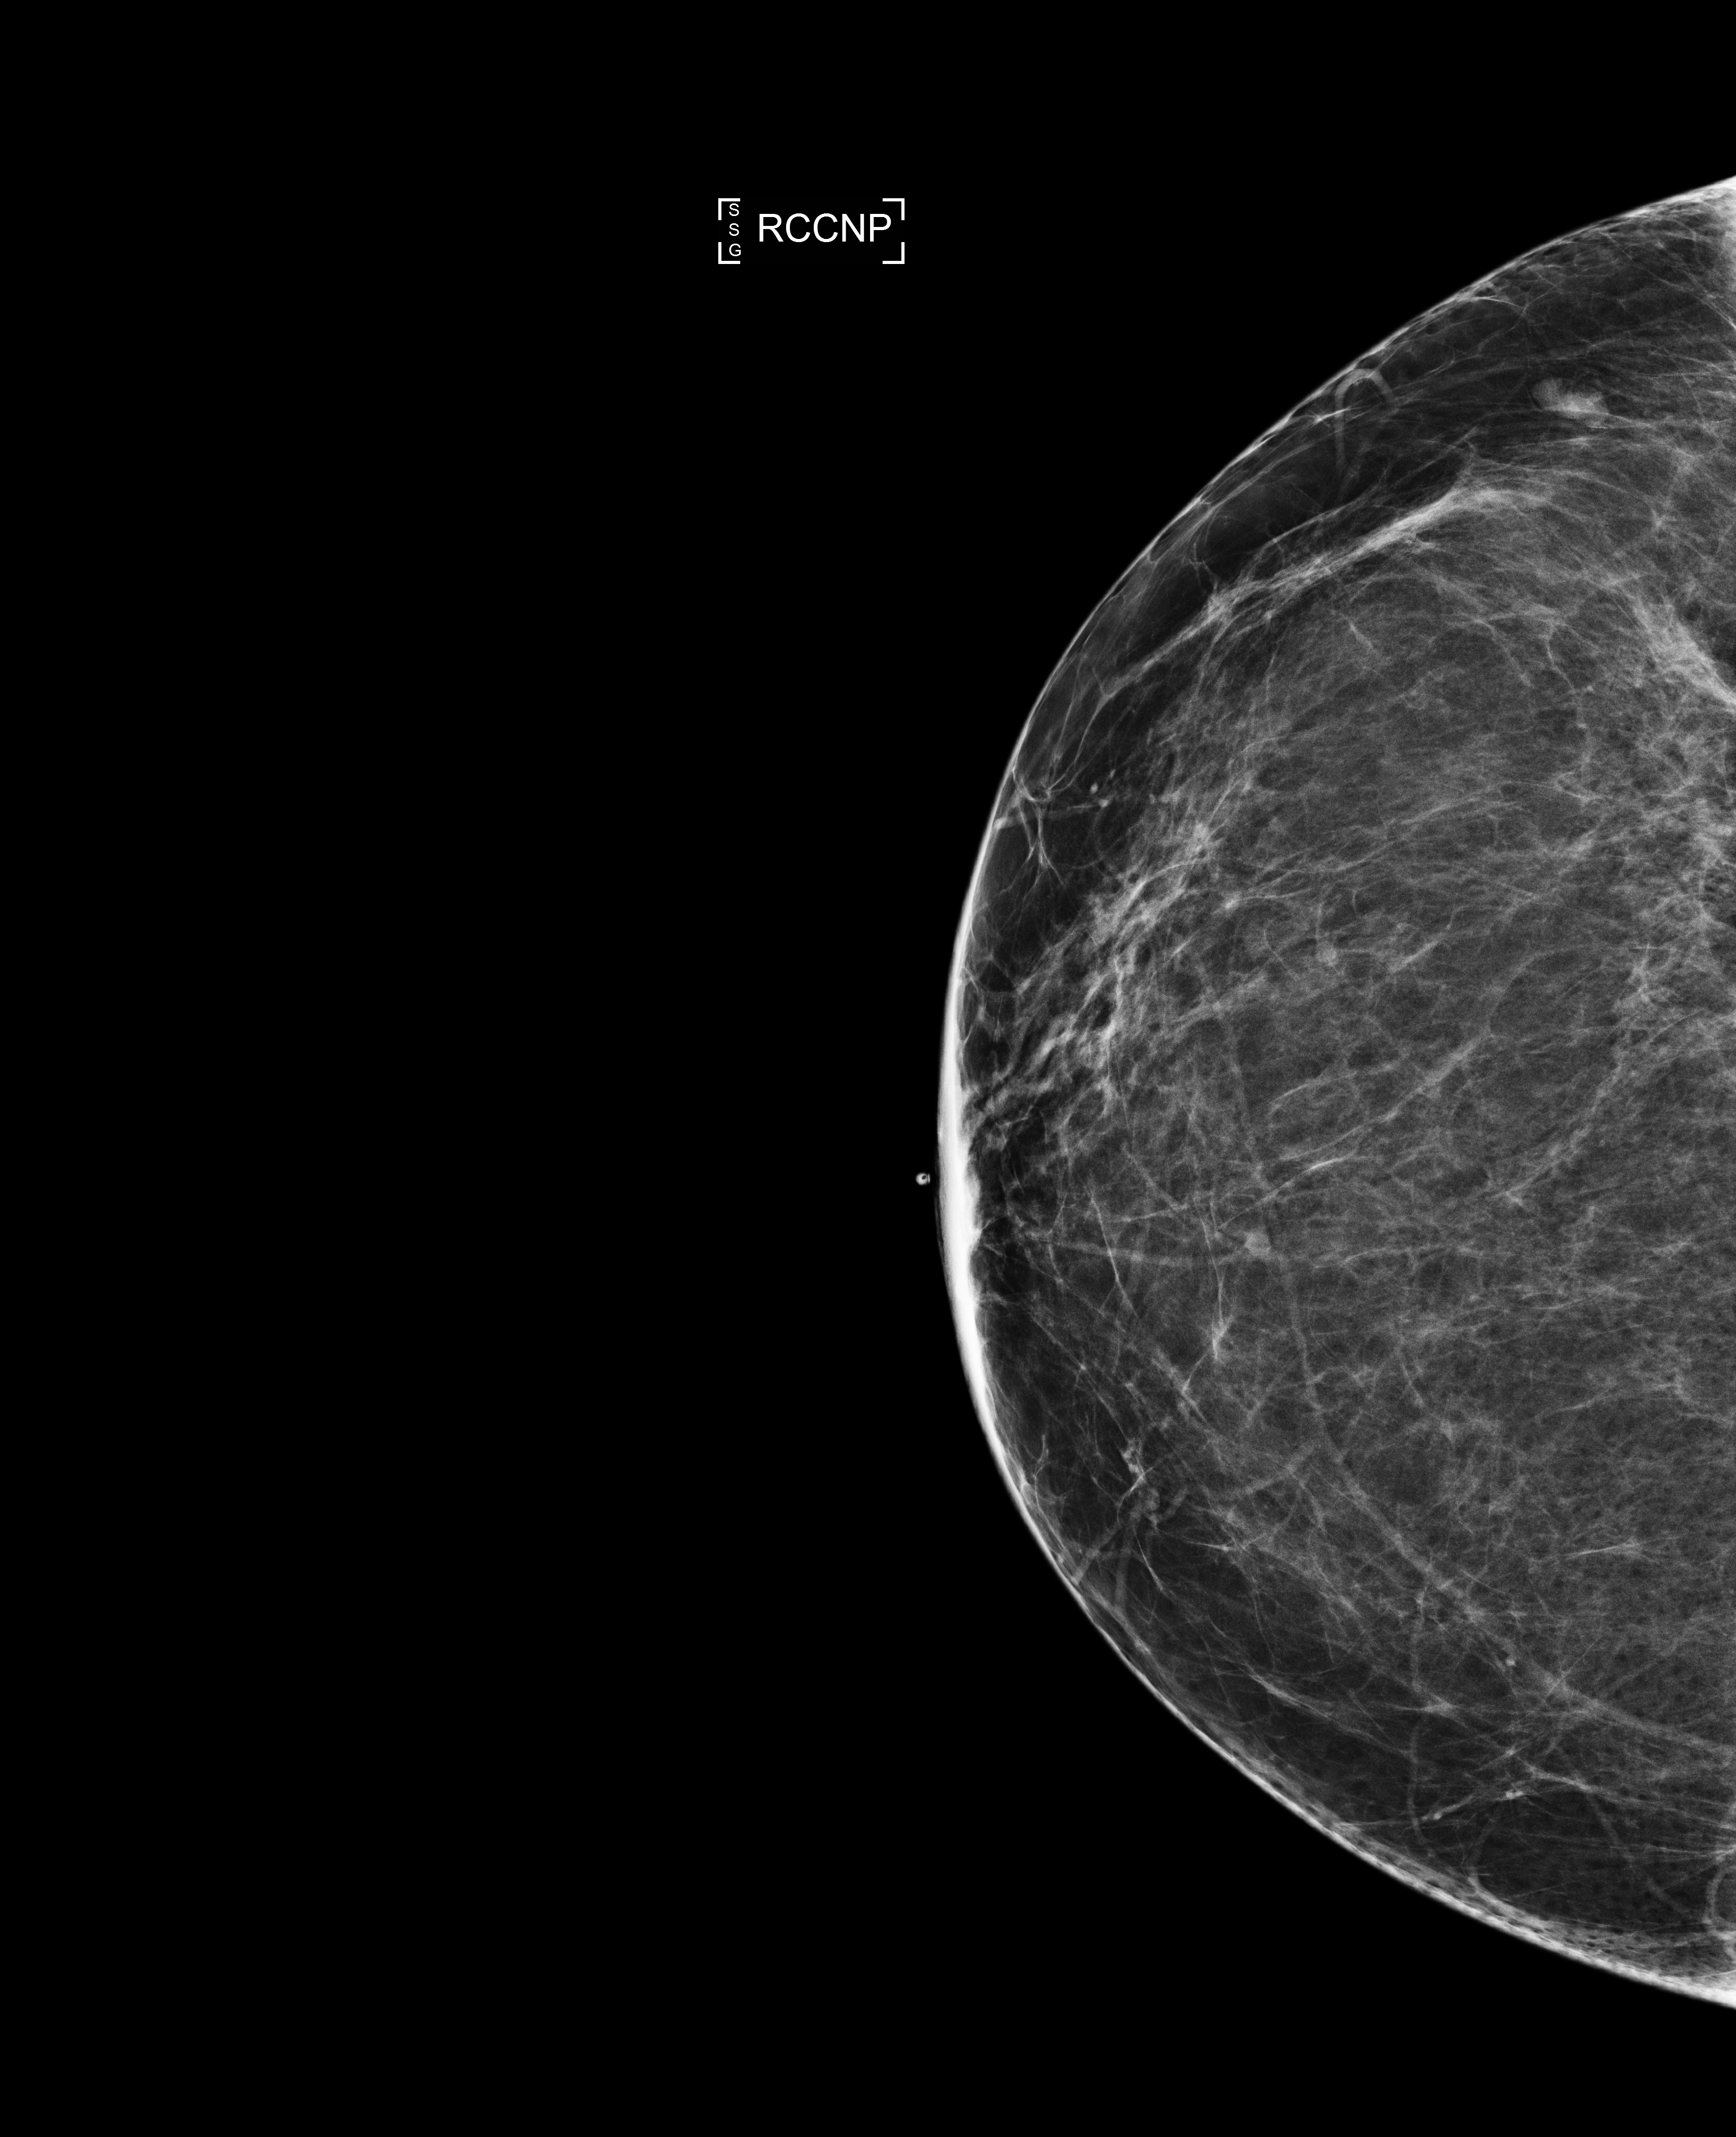
Annual screening mammography examination. Patient: female, 51 years.
Image type: full-field digital mammogram. Breast: right. Projection: cranio-caudal projection, nipple in profile. Breast density at the screening exam (both breasts): scattered fibroglandular densities (BI-RADS density category b). Final BI-RADS category for the screening round (tomosynthesis exam, both breasts): category 2. Recall: no recall after this screen.